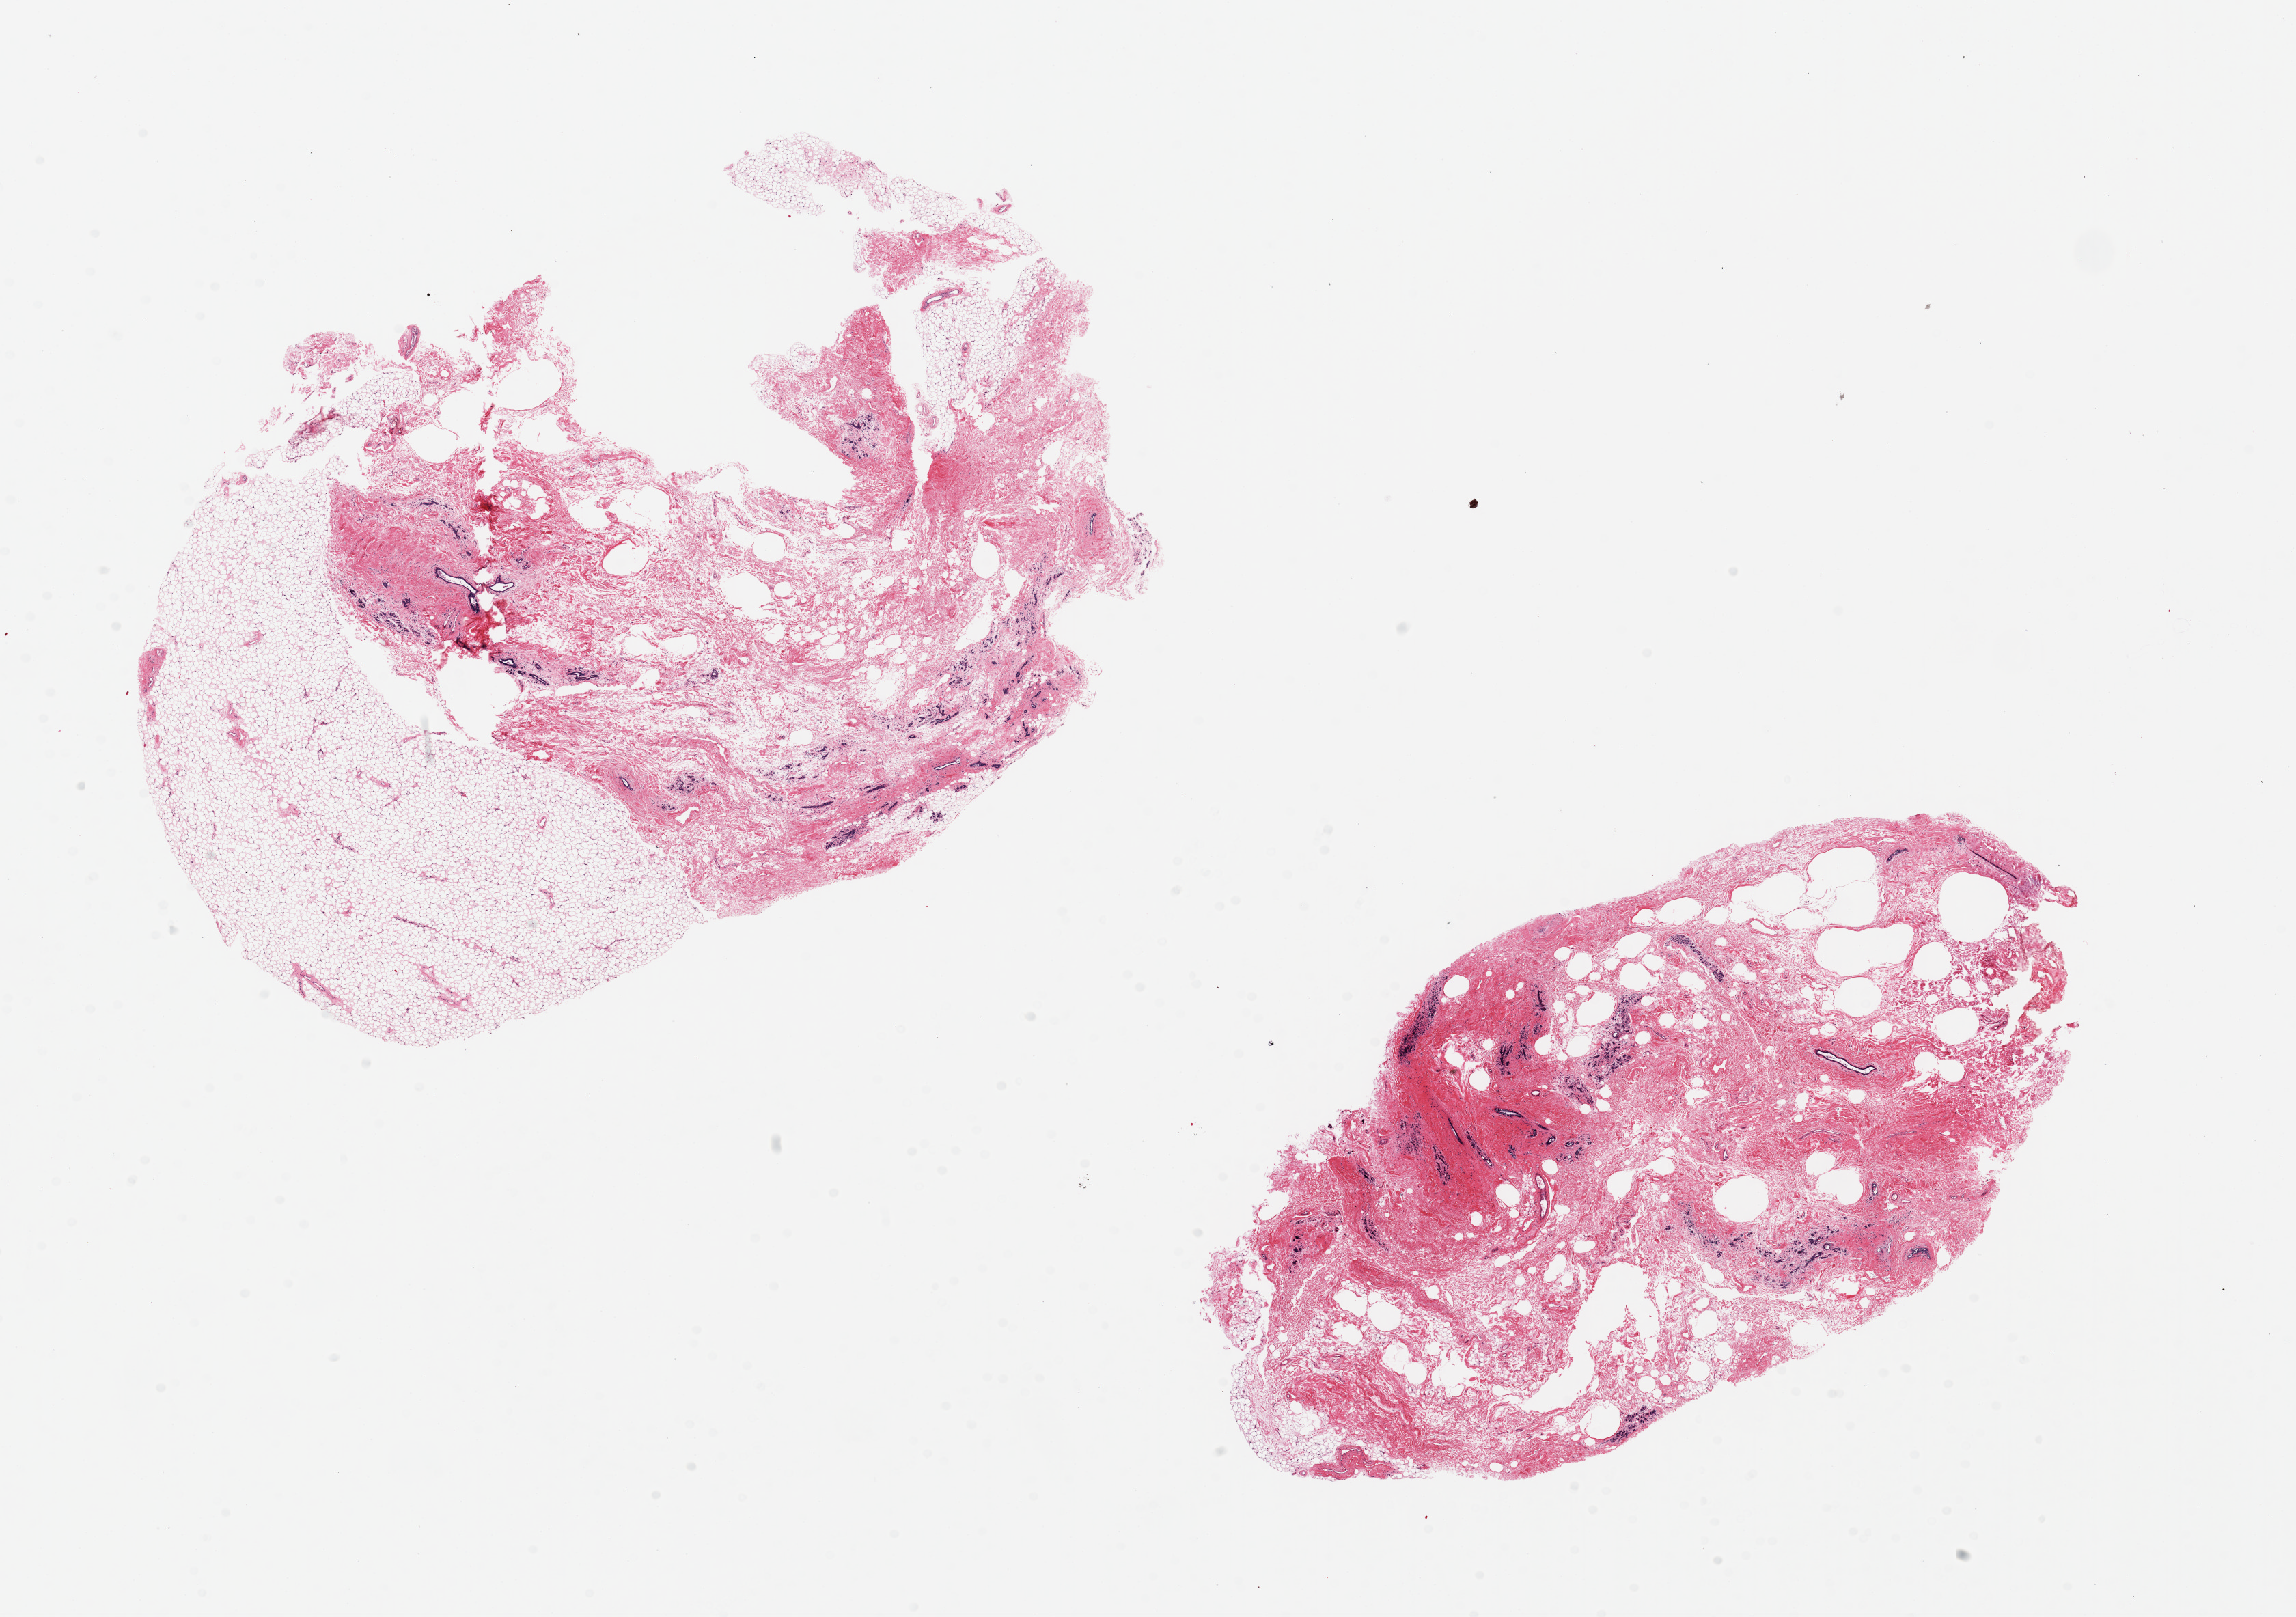
Hematoxylin and eosin (H&E) whole-slide image — a low-resolution overview of the entire scanned area, about 26.6 x 18.7 mm; PAXgene-fixed paraffin-embedded (PFPE) section; section of breast (target tissue); tissue donor sample. Female donor.
Pathologist's review note for this sample: 2 pieces, 13x9 & 11x6mm; atrophic glands in fibroadipose tissue.